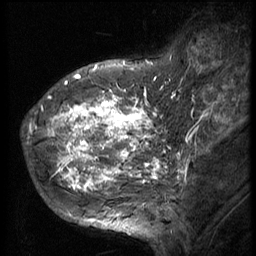
Breast MRI (dynamic contrast-enhanced), one sagittal slice; 3 images stored at this slice position (order not interpretable as contrast timing); 1.5 T; TE 4.2 ms, TR 9 ms; 2.5 mm slice thickness; 256 × 256 image matrix. Female patient, age 49 years. From the clinical record (not read from this slice): setting: breast cancer imaged before/during neoadjuvant chemotherapy; receptor status: HER2-positive.
Outlined on this slice (semi-automatic segmentation, software-assisted and operator-edited):
- analysis volume of interest (the breast-tissue region the enhancement analysis was run in; not a lesion): bounding box [x1, y1, x2, y2] px = [37, 85, 151, 207]
- tumour enhancement mask (voxels above the 140 % enhancement threshold inside the analysis volume of interest): [47, 85, 150, 192]